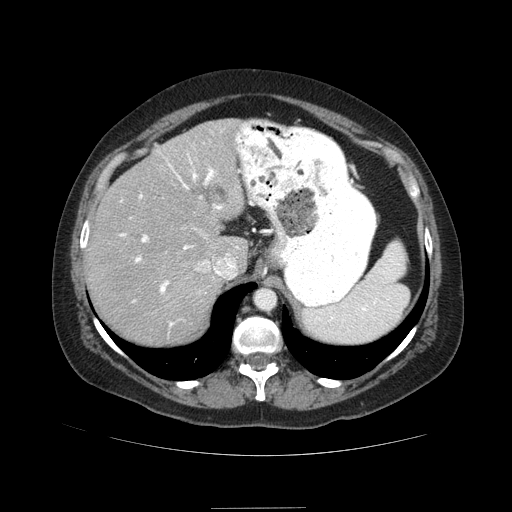
Contrast-enhanced abdominal CT (liver protocol), one axial slice; position 64 of 89 along the scan axis; 120 kVp; soft-tissue window (W 400 / L 40 HU); 512 × 512 image matrix, field of view 400 × 400 mm. From the clinical record (not read from this slice): diagnosis: hepatocellular carcinoma (patient treated with transarterial chemoembolisation; whether this scan precedes or follows treatment is not stated here); TNM stage (as recorded): Stage-IIIB; Child-Pugh class: A.
Annotated regions visible in this slice (semi-automatic segmentation, software-assisted and operator-edited):
- abdominal aorta: box from (x=256, y=289) to (x=276, y=309) px
- liver parenchyma outside the tumour (the mass and vessels are separate outlines, so this box may not span the whole liver): (x=86, y=118)–(x=244, y=344)
- liver vessels: (x=119, y=155)–(x=222, y=327)